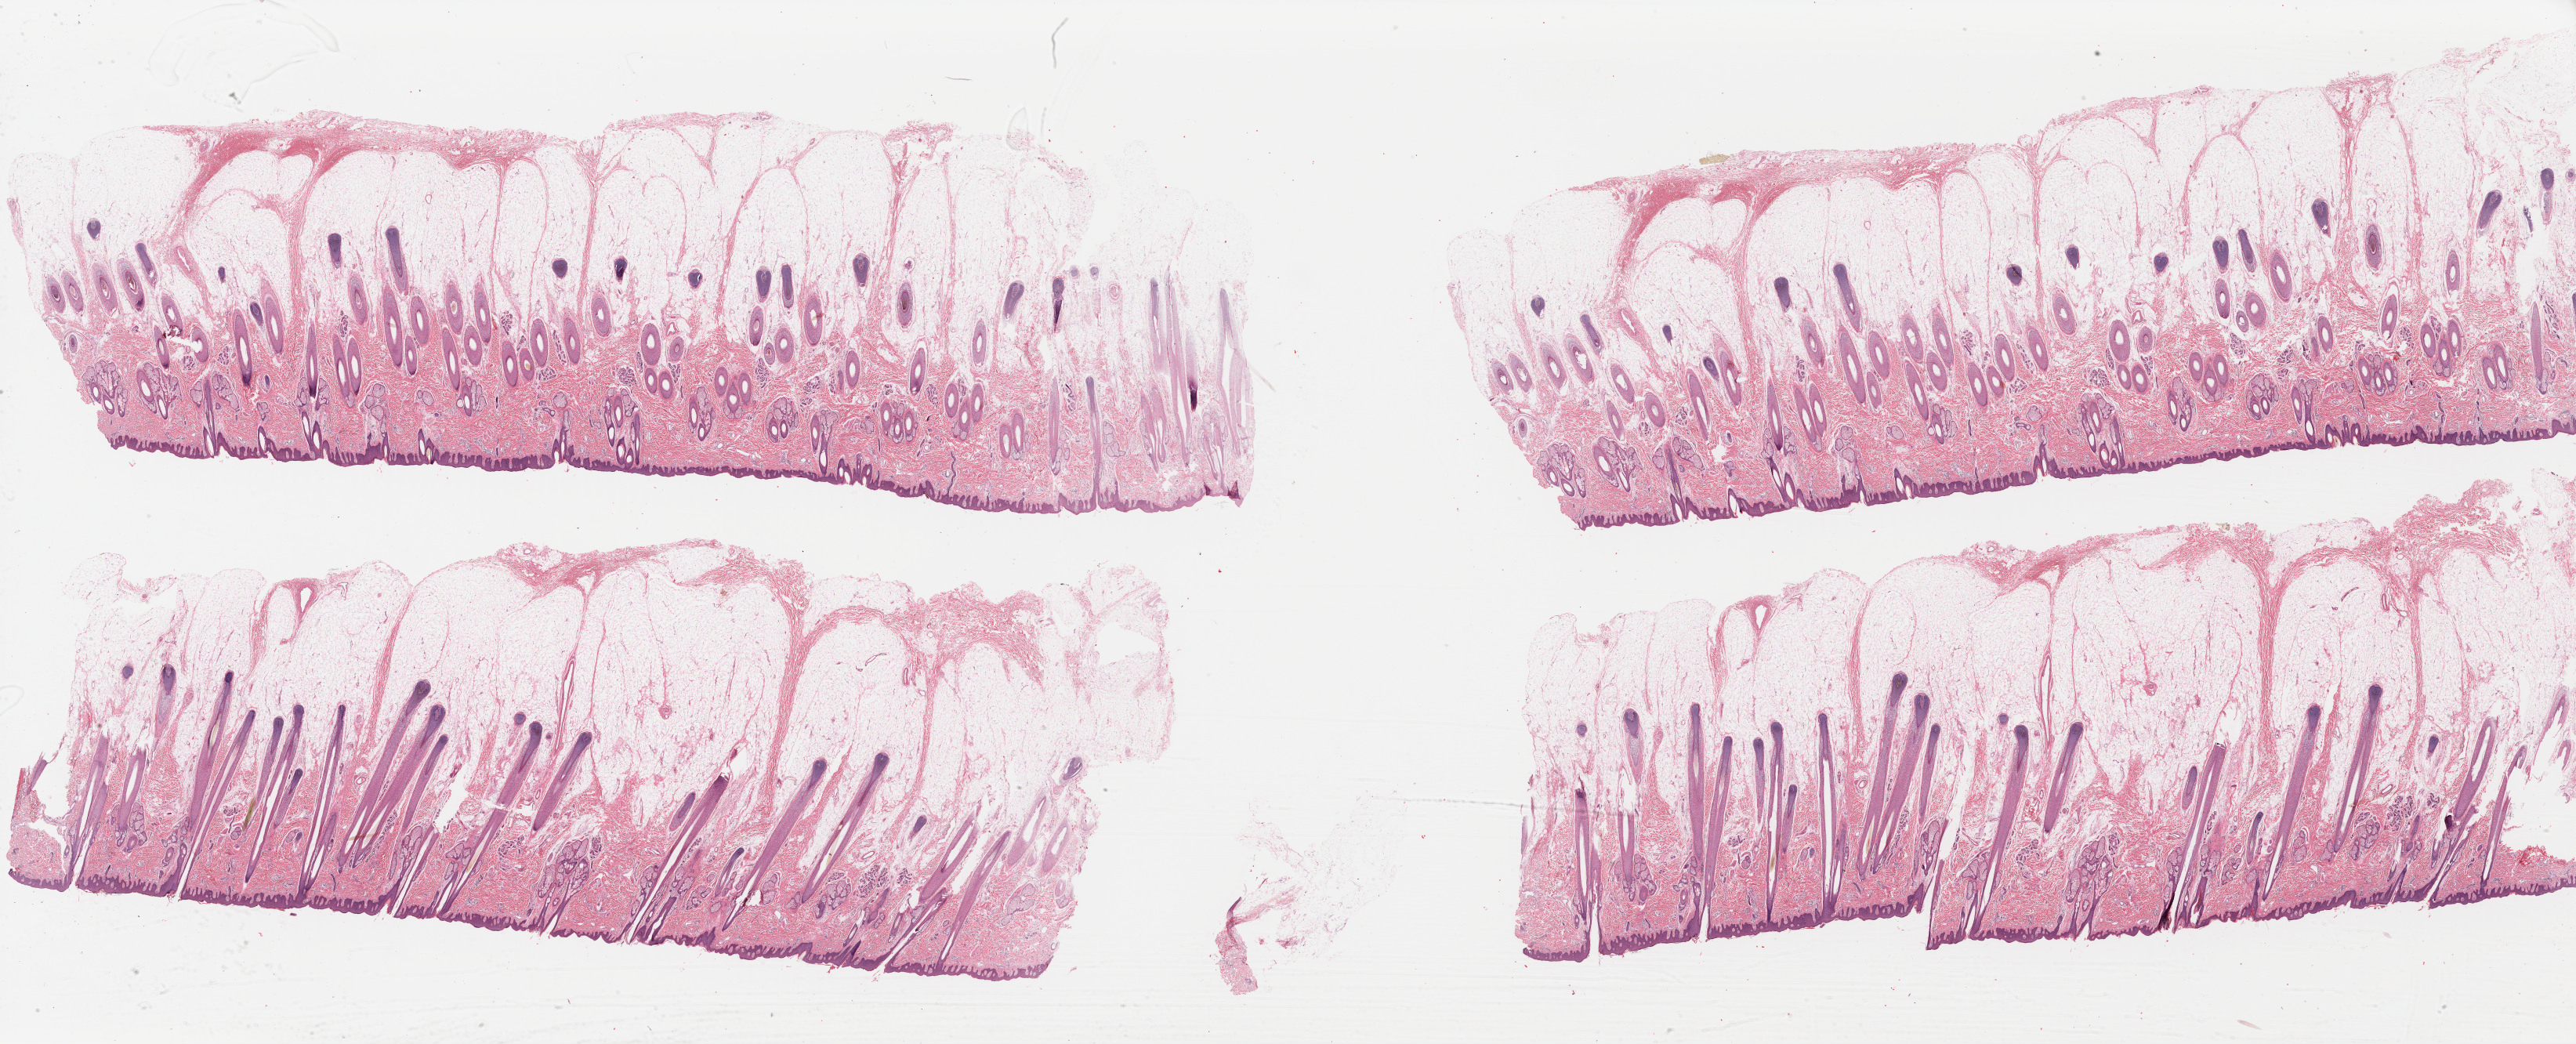
Digitized H&E tissue section (whole slide), low-resolution overview of the scanned area, about 51.7 x 20.9 mm (acquisition: 40x scan), formalin-fixed paraffin-embedded (FFPE) diagnostic section, metastatic tumour sample, sampled site not recorded. Male, age 19 years at initial diagnosis.
• this section: metastatic tumour tissue
• patient diagnosis: Malignant melanoma, NOS